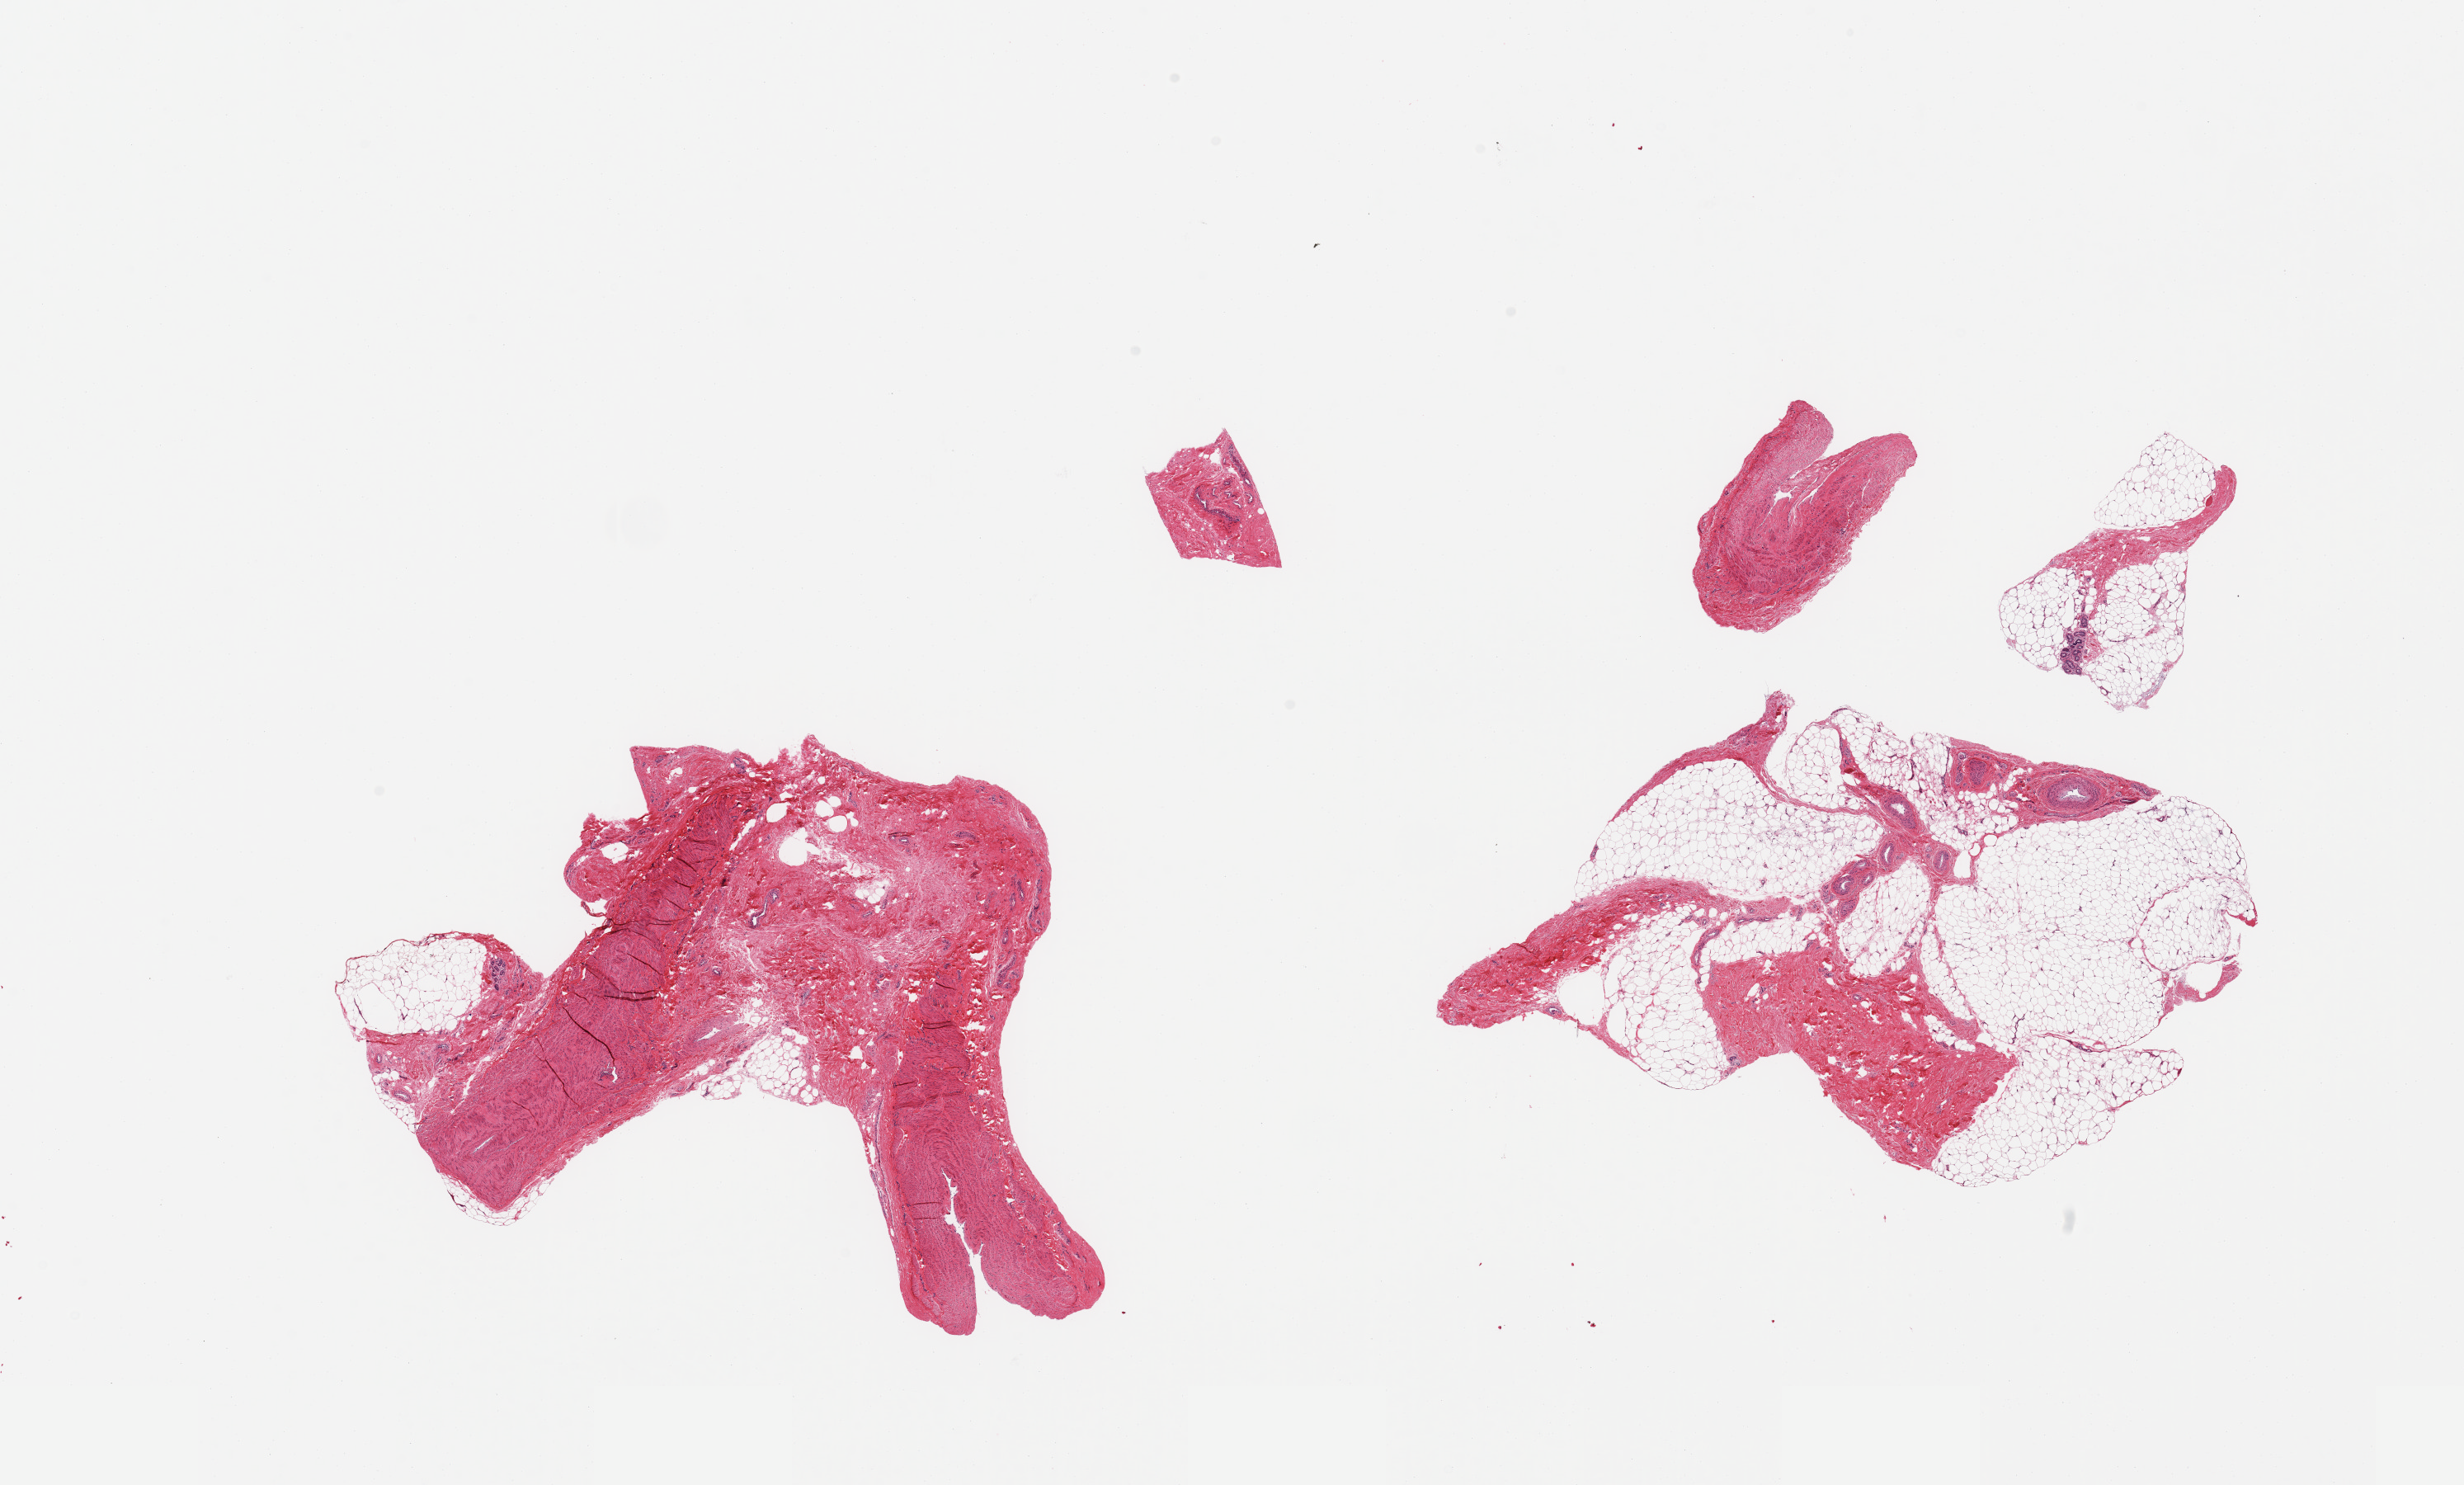
Haematoxylin and eosin whole-slide image, shown as a low-resolution overview of the whole scanned area (about 23.6 x 14.2 mm, acquisition: 20x scan). PAXgene-fixed, paraffin-embedded tissue. Sampled site (target tissue): adipose tissue. Tissue donor sample. Male donor.
Pathologist's review note for this sample: 5 pieces; two larger pieces consist of fibrovascular component and 5% and 60% mature adipose tissue; 2 of 3 smaller pieces represent fibrovascular tissue; the remaining one consists of adipose tissue with small fibrovascular component and adnexal ducts.